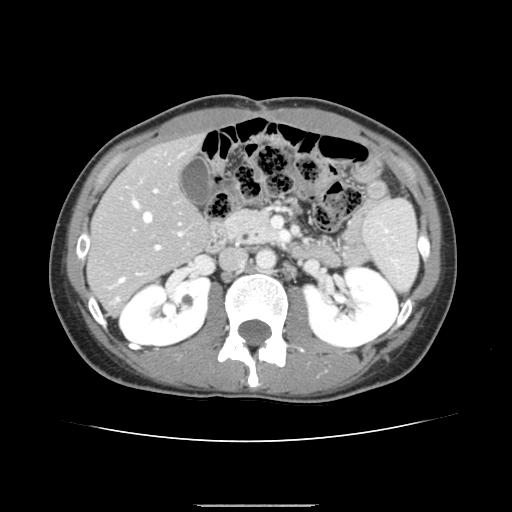
Contrast-enhanced abdominal CT, one axial slice. Slice 72 of 150 in the series (ordered by position). Intravenous contrast given. Soft-tissue window (W 400 / L 40 HU). 512 × 512 image matrix, field of view 324 × 324 mm. Female patient, age 32 years. From the clinical record (not read from this slice): diagnosis: colorectal cancer liver metastases, imaged before liver resection; multiple liver metastases: yes; largest metastasis: 0.7 cm; chemotherapy before resection: yes.
Outlined on this slice (outlined manually by an expert reader):
- hepatic veins: box from (x=120, y=201) to (x=181, y=282) px
- liver: (x=89, y=137)–(x=207, y=313)
- planned liver remnant (the part of the liver to remain after resection): (x=89, y=137)–(x=208, y=284)
- portal vein (with intrahepatic branches): (x=115, y=189)–(x=180, y=302)